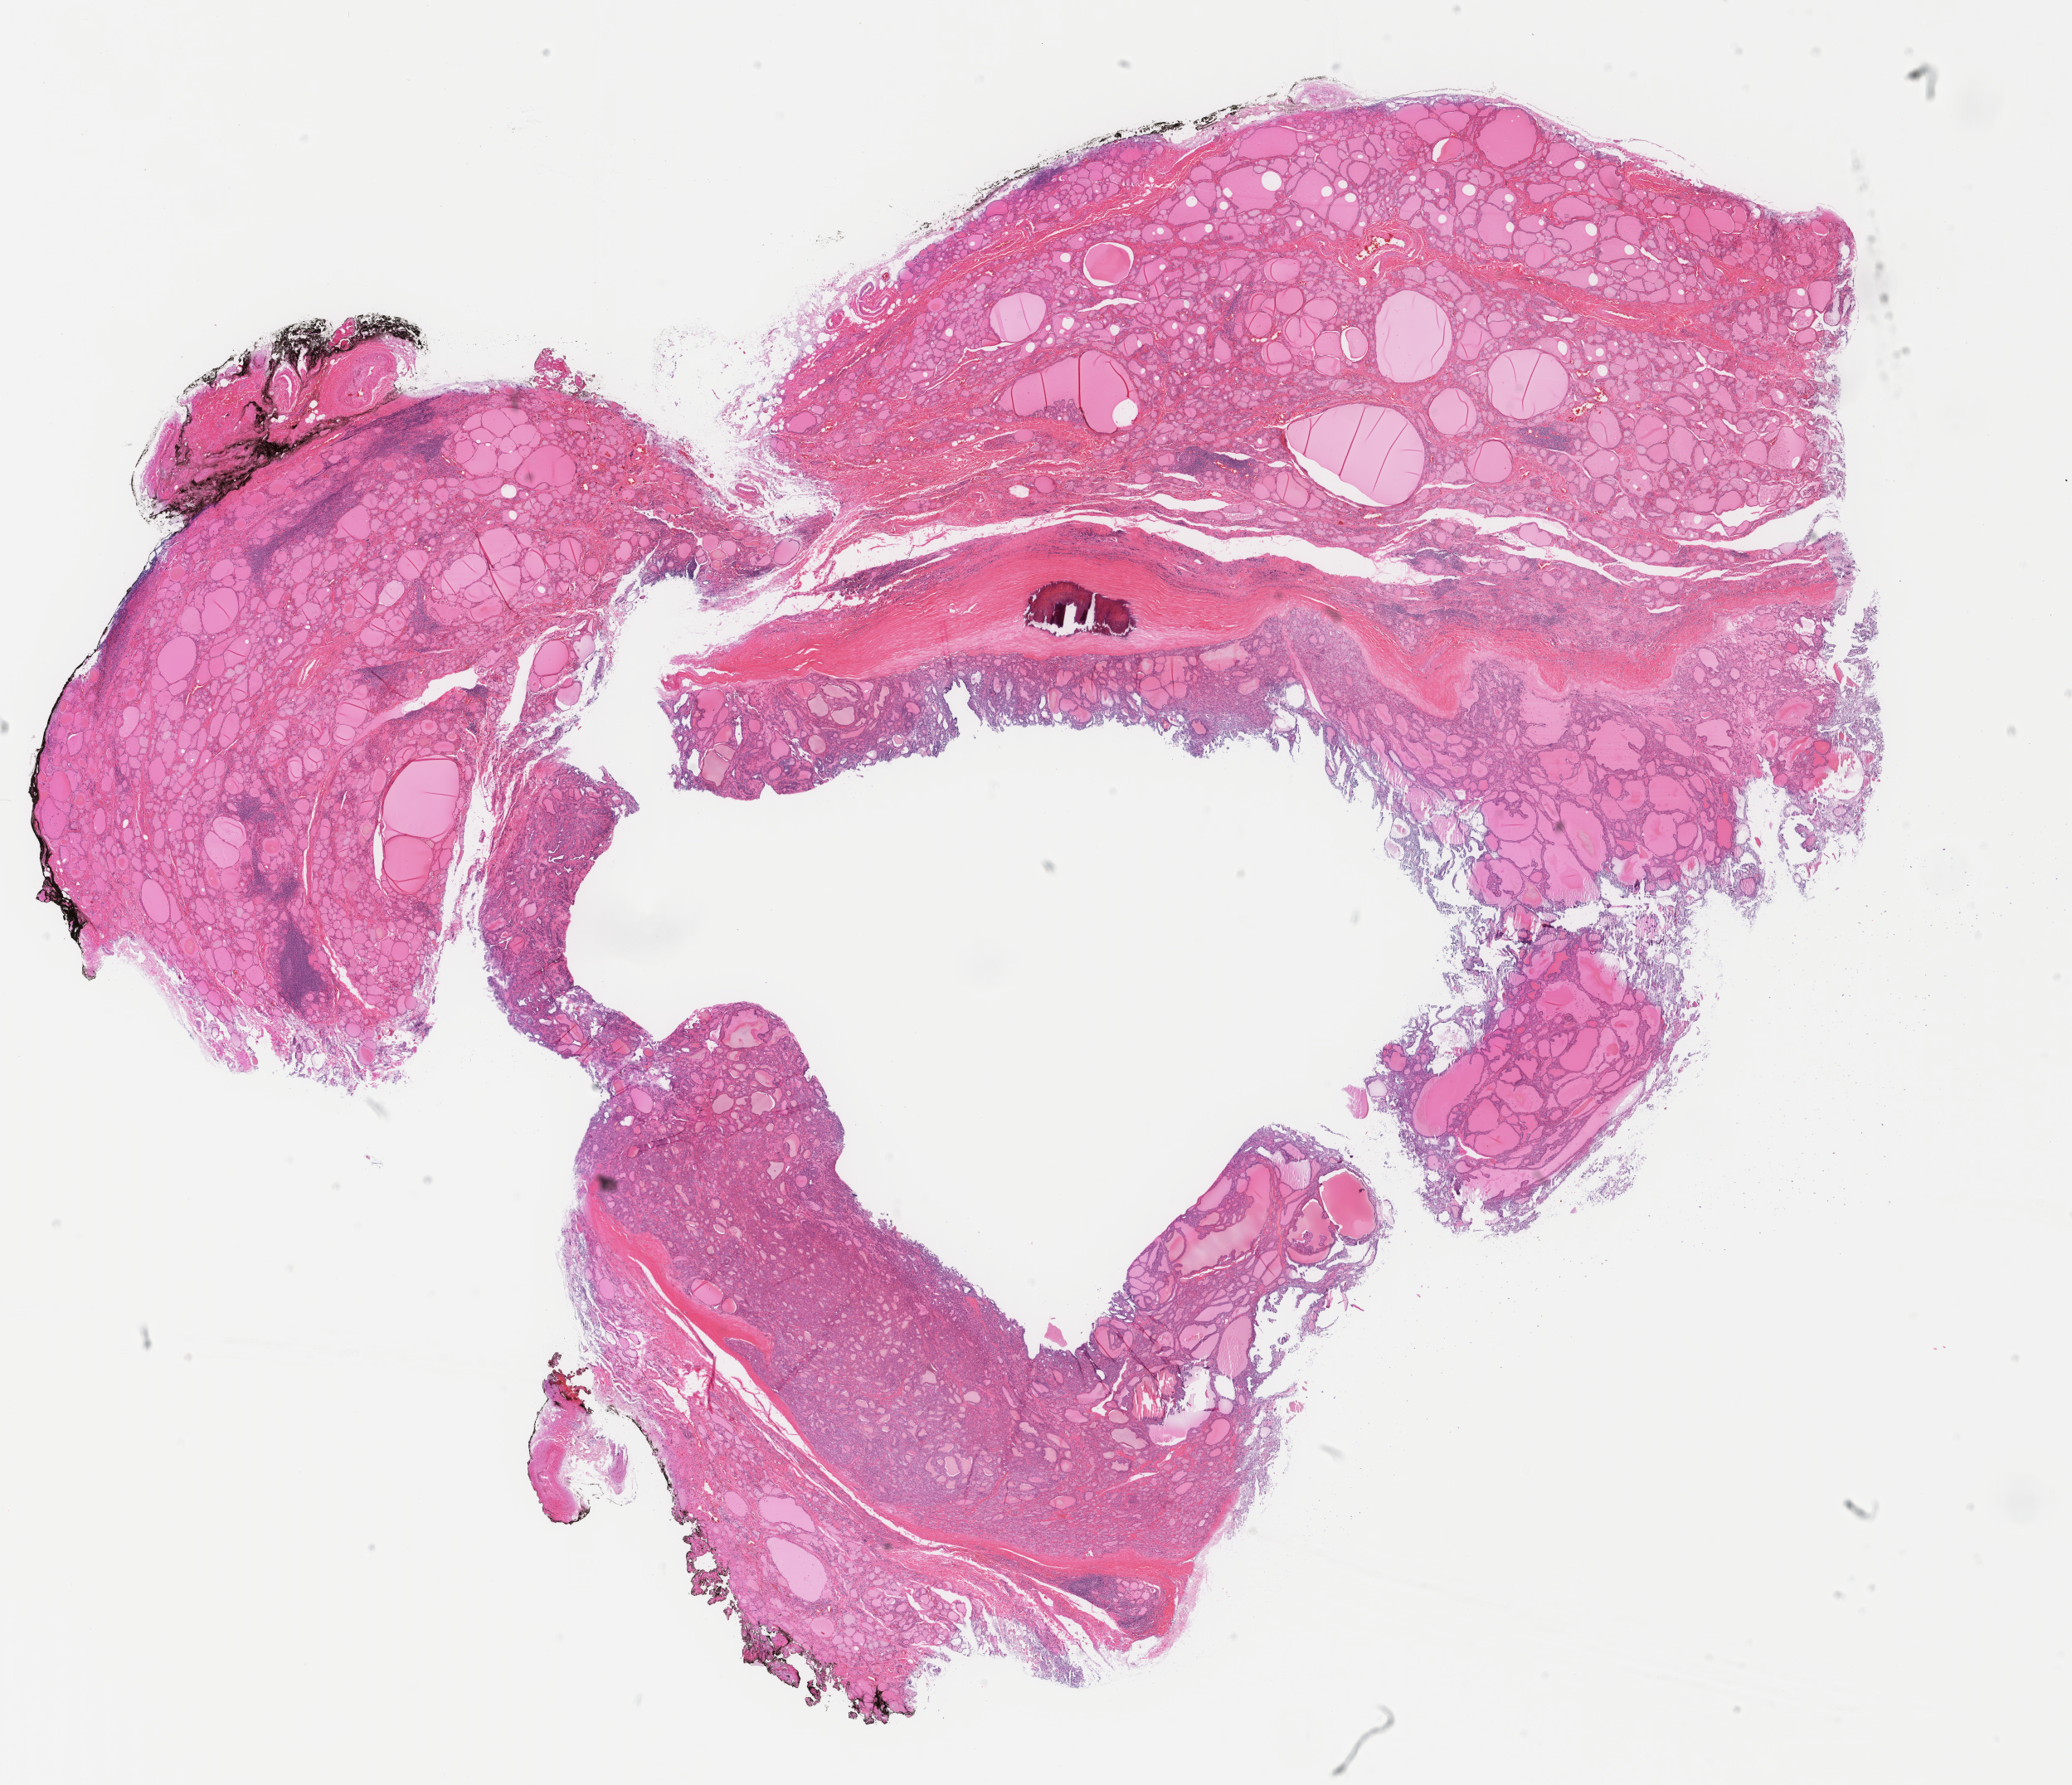
Digitized Hematoxylin and eosin (H&E) stained tissue section (whole slide), whole scanned area (about 19.8 x 17.1 mm) shown as a low-resolution overview, formalin-fixed paraffin-embedded (FFPE) diagnostic section, thyroid, primary tumour sample. Patient: female, age at initial diagnosis 66 years.
AJCC pathologic stage: I (4th edition). Pathologic diagnosis: Papillary adenocarcinoma, NOS (thyroid gland).